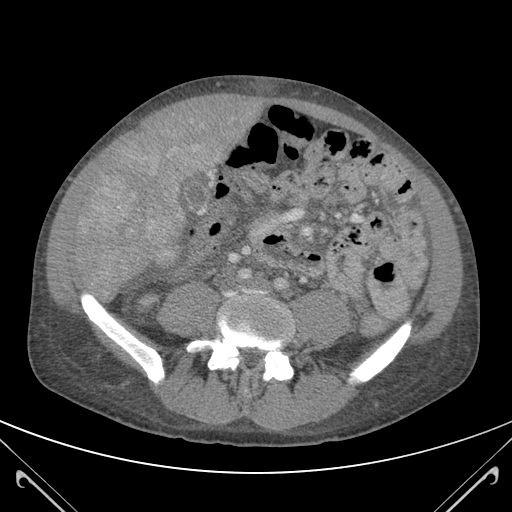
Contrast-enhanced abdominal CT (liver protocol), one axial slice; slice 30 of 118 in the series (ordered by position); soft-tissue window (W 400 / L 40 HU); 3 mm slice thickness; 512 × 512 image matrix. From the clinical record (not read from this slice): diagnosis: hepatocellular carcinoma (patient treated with transarterial chemoembolisation; whether this scan precedes or follows treatment is not stated here); TNM stage (as recorded): Stage-IIIB; Child-Pugh class: A; tumour nodularity: uninodular.
Annotated regions visible in this slice (semi-automatic segmentation, software-assisted and operator-edited):
- mass: bounding box (x1, y1, x2, y2) in pixels: (80, 95, 245, 272)